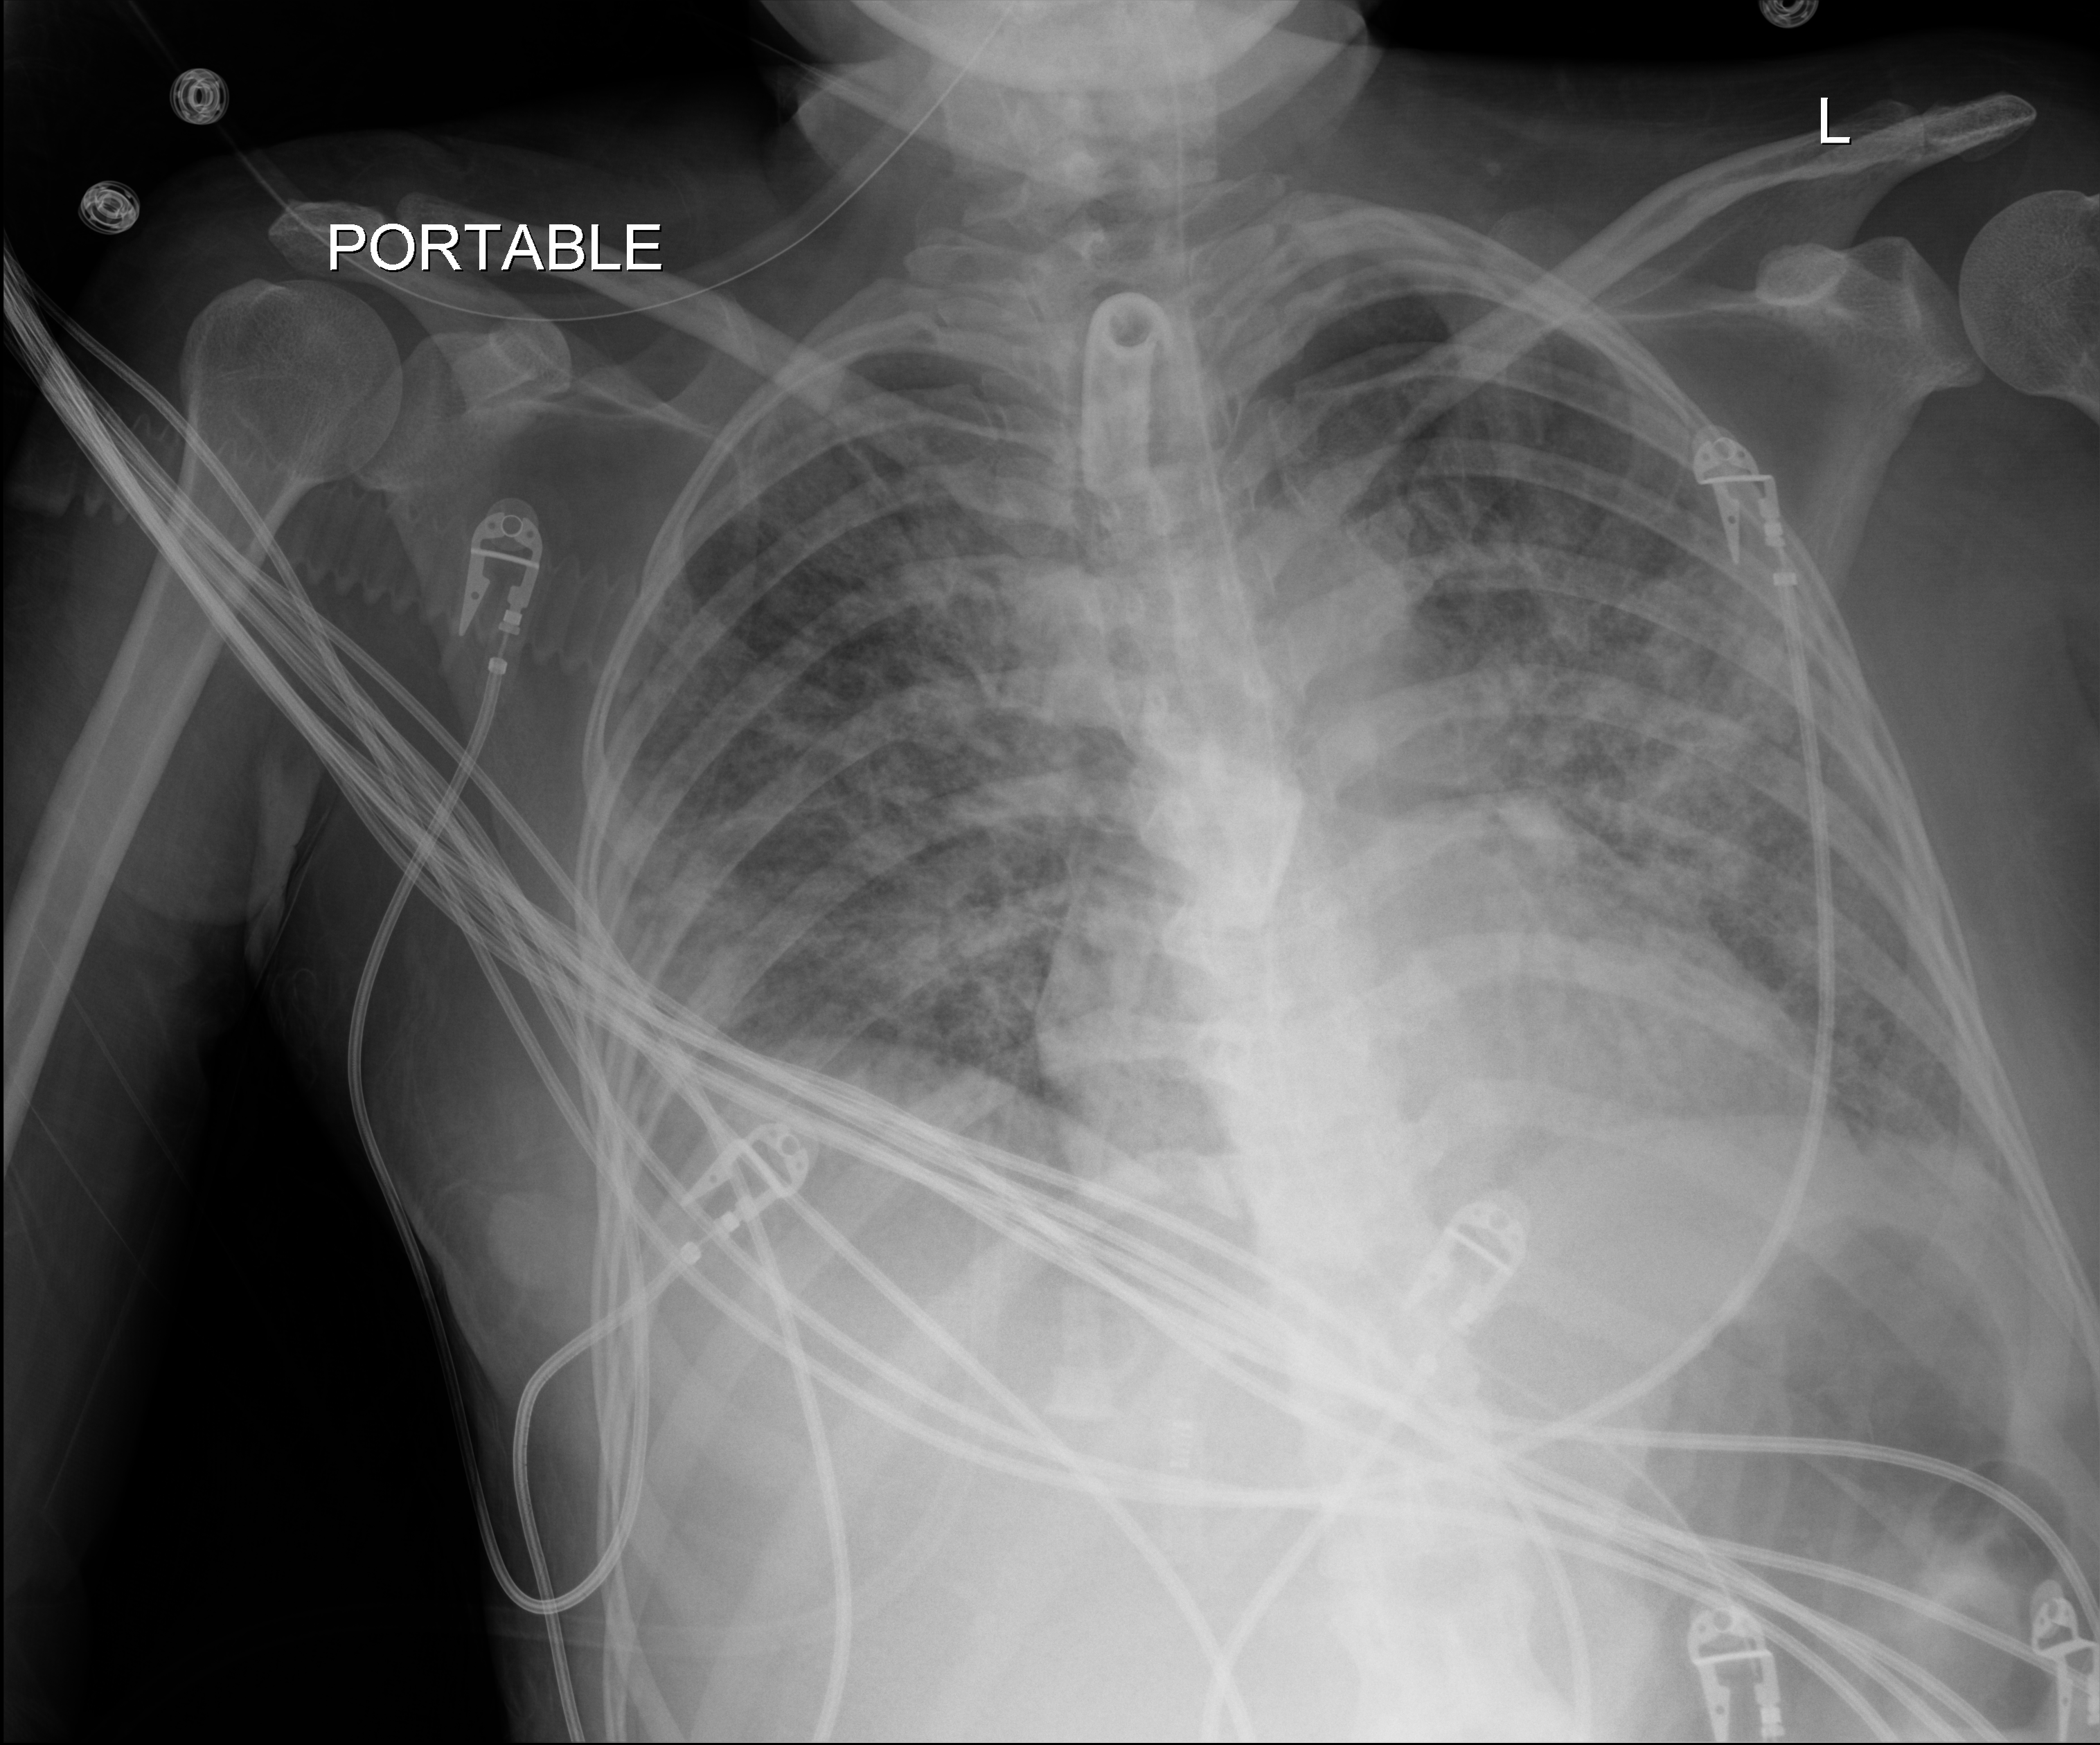
Portable chest radiograph; anteroposterior (AP) projection. Female patient hospitalised with COVID-19, age 18–59 years.
Hospital-stay facts (about this admission, not read from this image; timing relative to this image not recorded): length of hospital stay: 71 days; chronic kidney disease (admission record): no; mechanically ventilated during this hospital stay: yes.